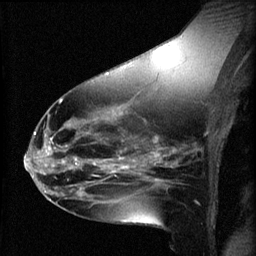
Breast MRI (dynamic contrast-enhanced), one sagittal slice; slice 31 of 60 in the series (ordered by position); 3 images stored at this slice position (order not interpretable as contrast timing); 1.5 T; TE 4.2 ms, TR 8.2 ms; 2 mm slice thickness; 256 × 256 image matrix. Patient: female, 49 years.
Structures marked on this image (semi-automatic segmentation, software-assisted and operator-edited):
- analysis volume of interest (the breast-tissue region the enhancement analysis was run in; not a lesion): box from (x=45, y=136) to (x=109, y=187) px
- tumour enhancement mask (voxels above the 70 % enhancement threshold inside the analysis volume of interest): (x=45, y=136)–(x=109, y=187)